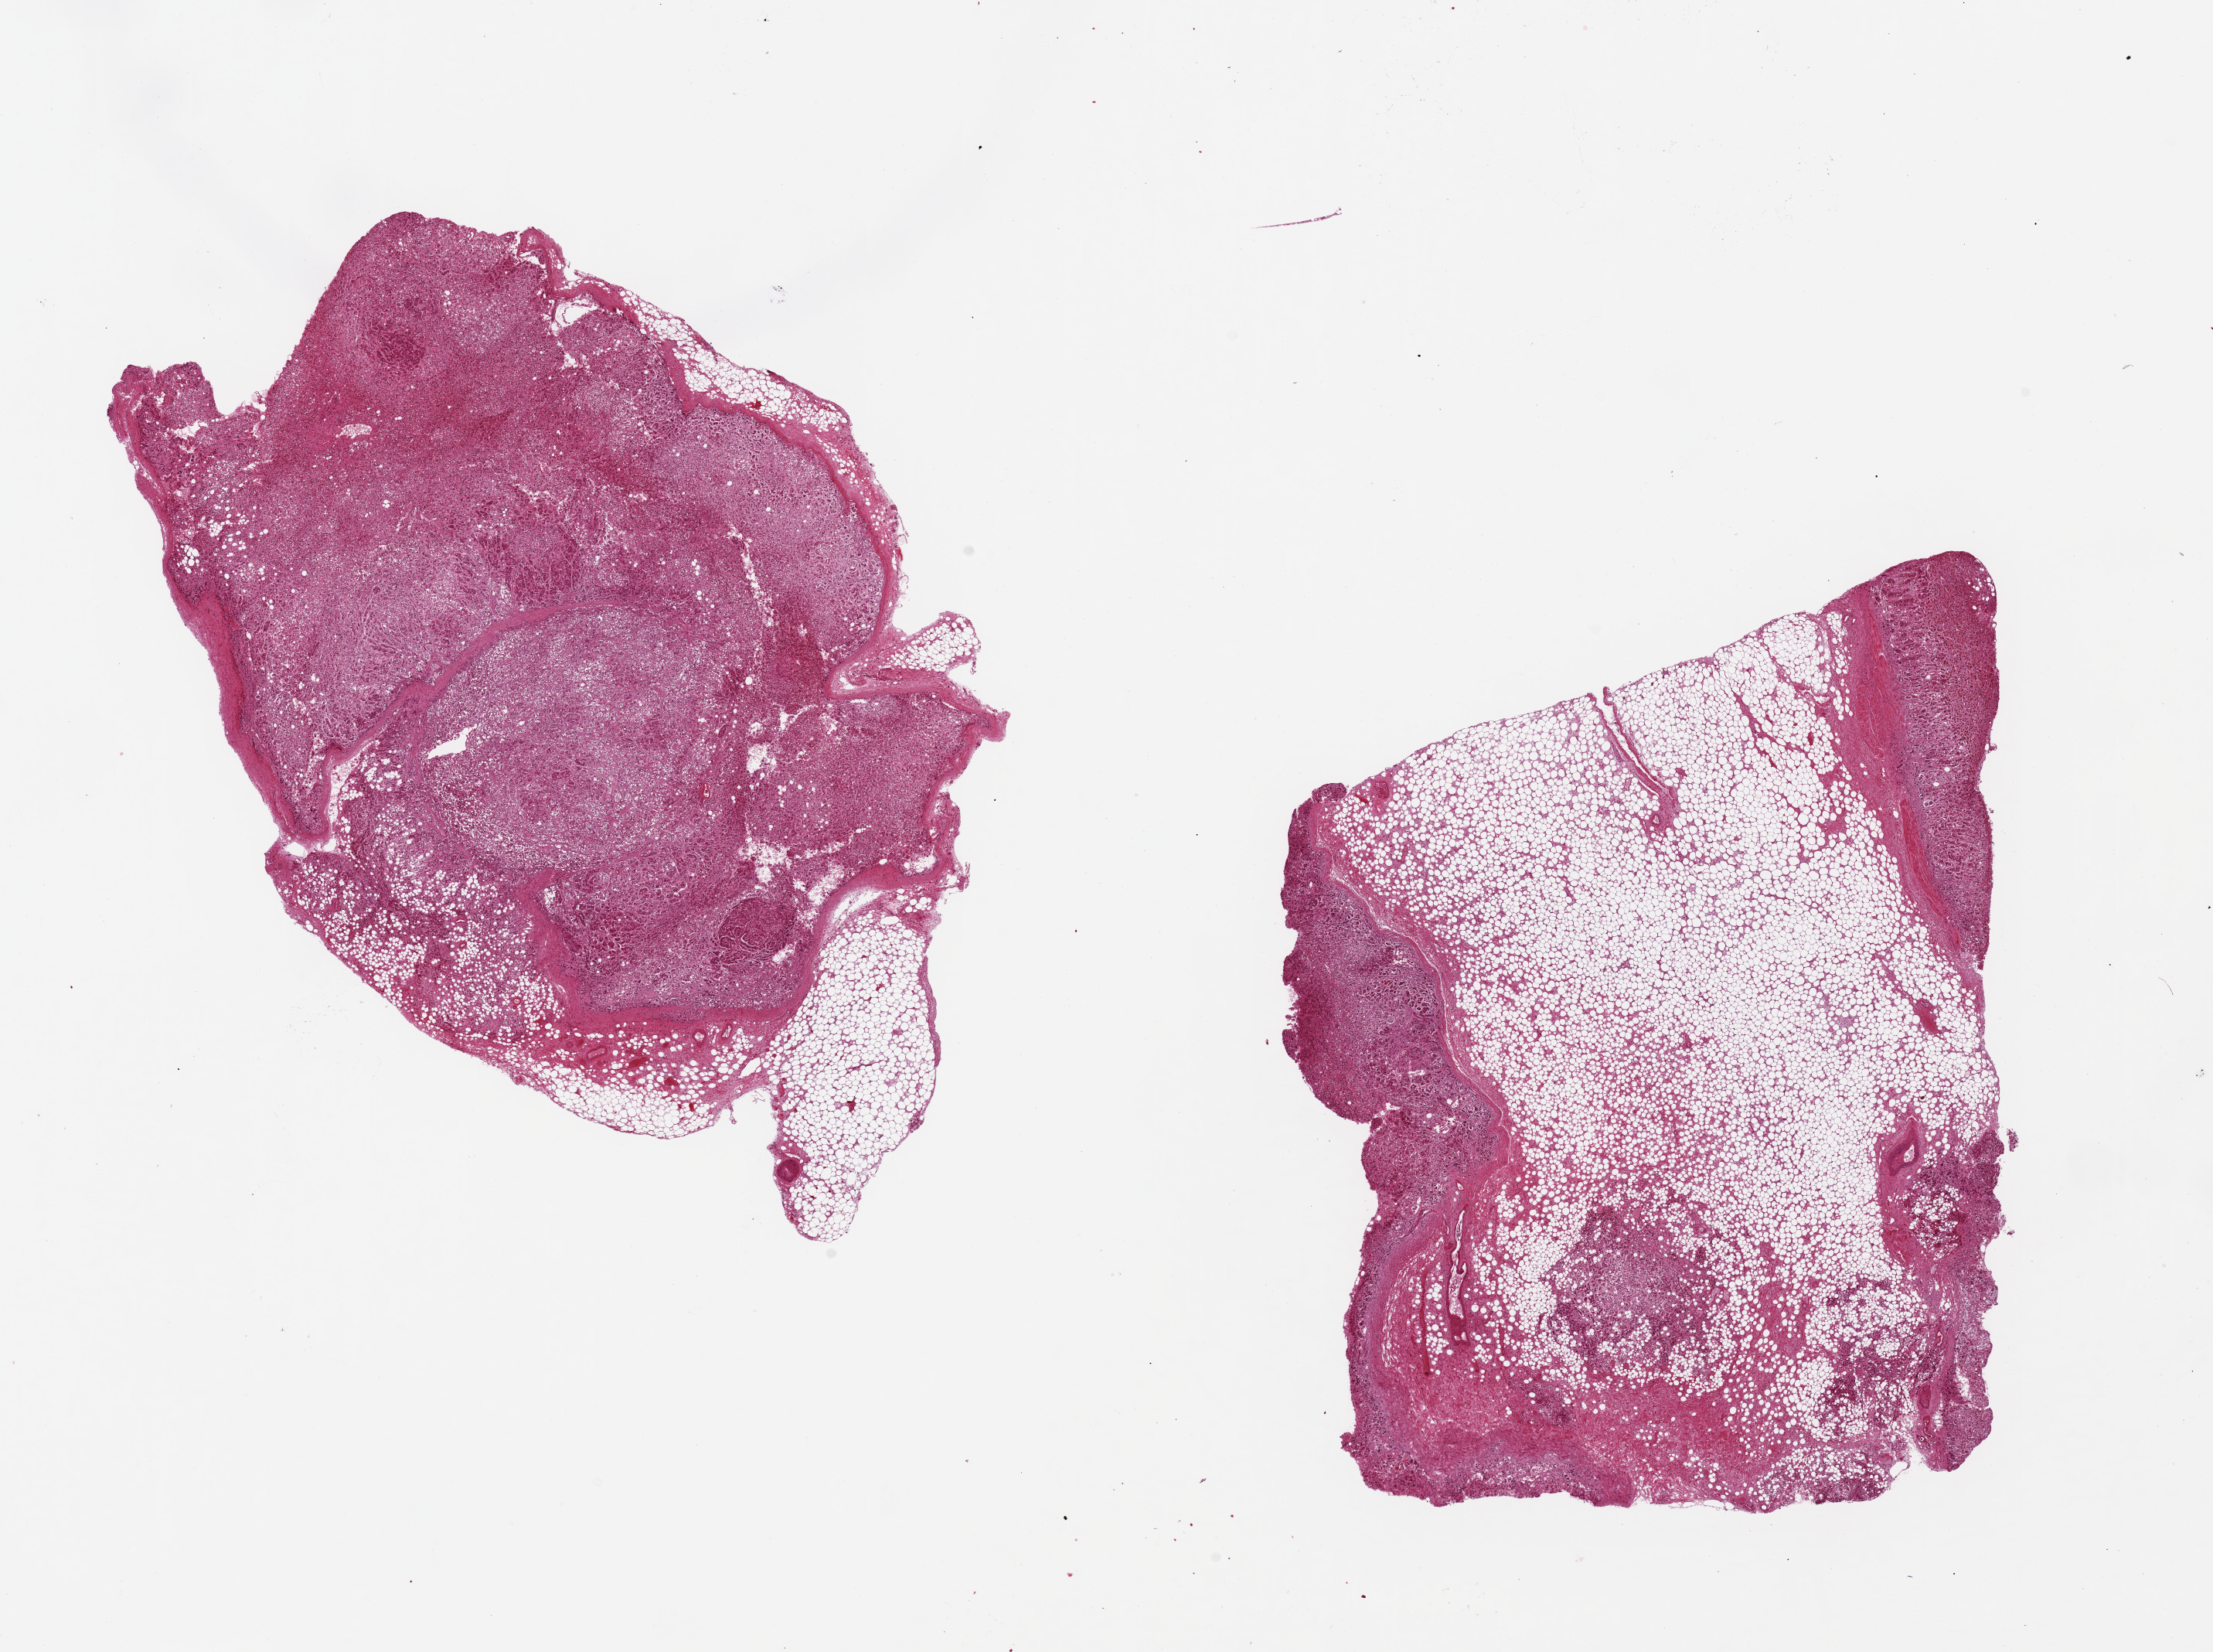
H&E whole-slide image, whole scanned area (about 22.6 x 16.9 mm, from a 20x scan) shown as a low-resolution overview, PAXgene-fixed paraffin-embedded (PFPE) section, section of adrenal gland (target tissue), donor tissue sample. Donor sex: male.
Review note (as recorded): 2 pieces, 11x8 & 10x8mm; 1 is 90% adipose; other is 20% adipose.